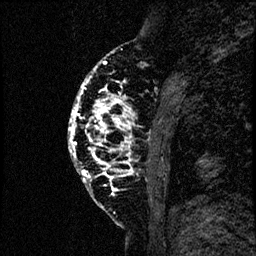
Breast MRI (dynamic contrast-enhanced), one sagittal slice; position 23 of 60 along the scan axis; dynamic contrast-enhanced study with each time point stored as its own series, time point 2 of 4 at this slice position (early post-contrast, ordered by acquisition time); 1.5 T; TE 4.2 ms, TR 17.6 ms; 2 mm slice thickness; 256 × 256 image matrix, field of view 200 × 200 mm. Female patient, age 40 years. From the clinical record (not read from this slice): setting: breast cancer imaged before/during neoadjuvant chemotherapy; receptor status: HER2-positive.
Outlined on this slice (semi-automatic segmentation, software-assisted and operator-edited):
- analysis volume of interest (the breast-tissue region the enhancement analysis was run in; not a lesion): bounding box [x1, y1, x2, y2] px = [66, 55, 184, 206]
- tumour enhancement mask (voxels above the 100 % enhancement threshold inside the analysis volume of interest): [68, 61, 130, 183]